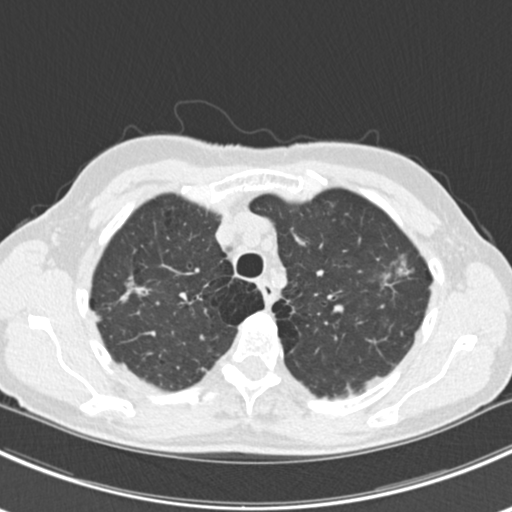
Chest CT (low-dose screening protocol), one axial image; first (baseline) screen; lung window (W 1500 / L -600 HU). Female participant, aged 63 years at enrolment. Current smoker at enrolment.
- Expert-annotated lung lesion, bounding box <365,242,433,311> (left, top, right, bottom; pixels).
- The screening reader recorded 10 non-calcified nodules or masses ≥4 mm on this exam (right lower lobe, right lower lobe, left lower lobe, left lower lobe, right middle lobe, right lower lobe, left lower lobe, left upper lobe, right upper lobe, left upper lobe); which of them this box marks is not recorded.